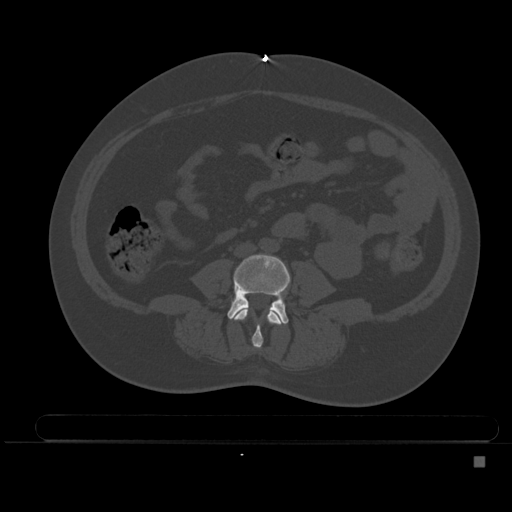
CT including the spine, one axial slice; bone window (W 1800 / L 400 HU); 1.5 mm slice thickness; 512 × 512 image matrix. Female patient, age 33 years. From the clinical record (not read from this slice): primary cancer: breast; vertebrae with lytic lesions (as recorded): T1.
Annotated regions visible in this slice (semi-automatic segmentation, software-assisted and operator-edited):
- L3 vertebra: bounding box [x1, y1, x2, y2] px = [234, 308, 283, 349]
- L4 vertebra: [227, 253, 290, 324]